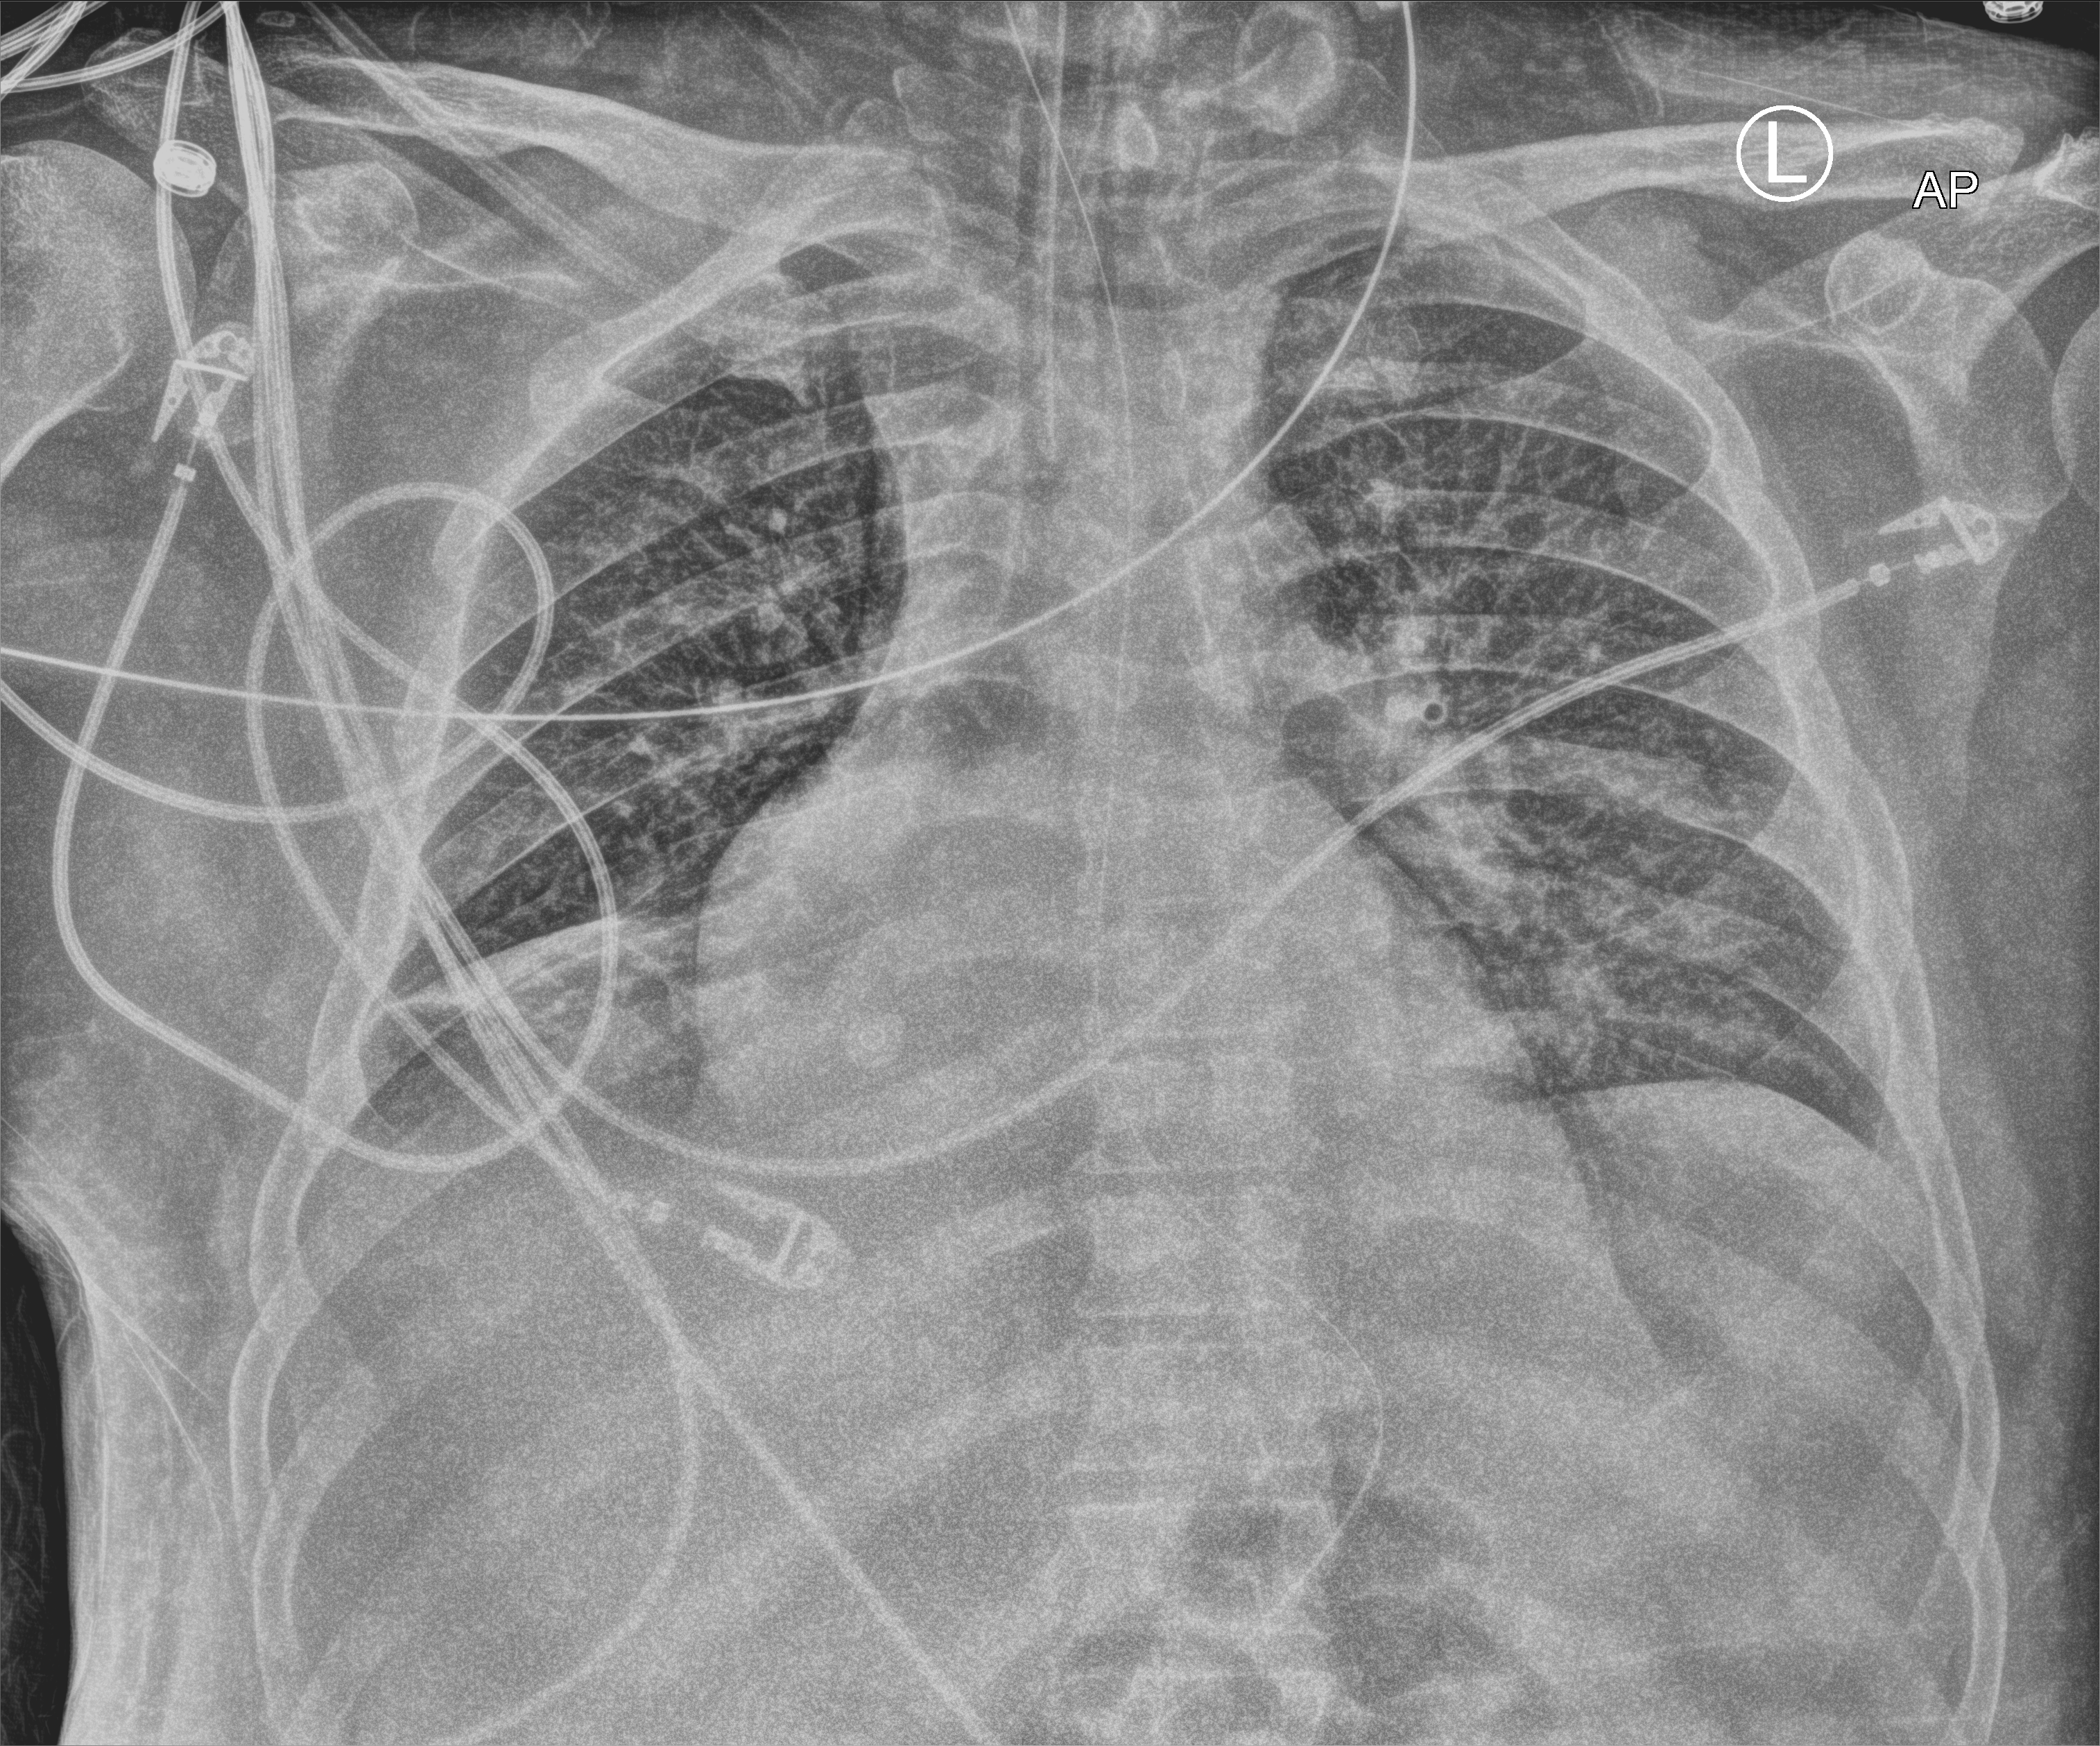
Bedside chest radiograph (computed radiography), anteroposterior (AP) projection. Male patient hospitalised with COVID-19, age 18–59 years.
From the hospital-stay record, not from the radiograph (when in the stay this image was taken is not recorded): admitted to intensive care during this hospital stay: yes.